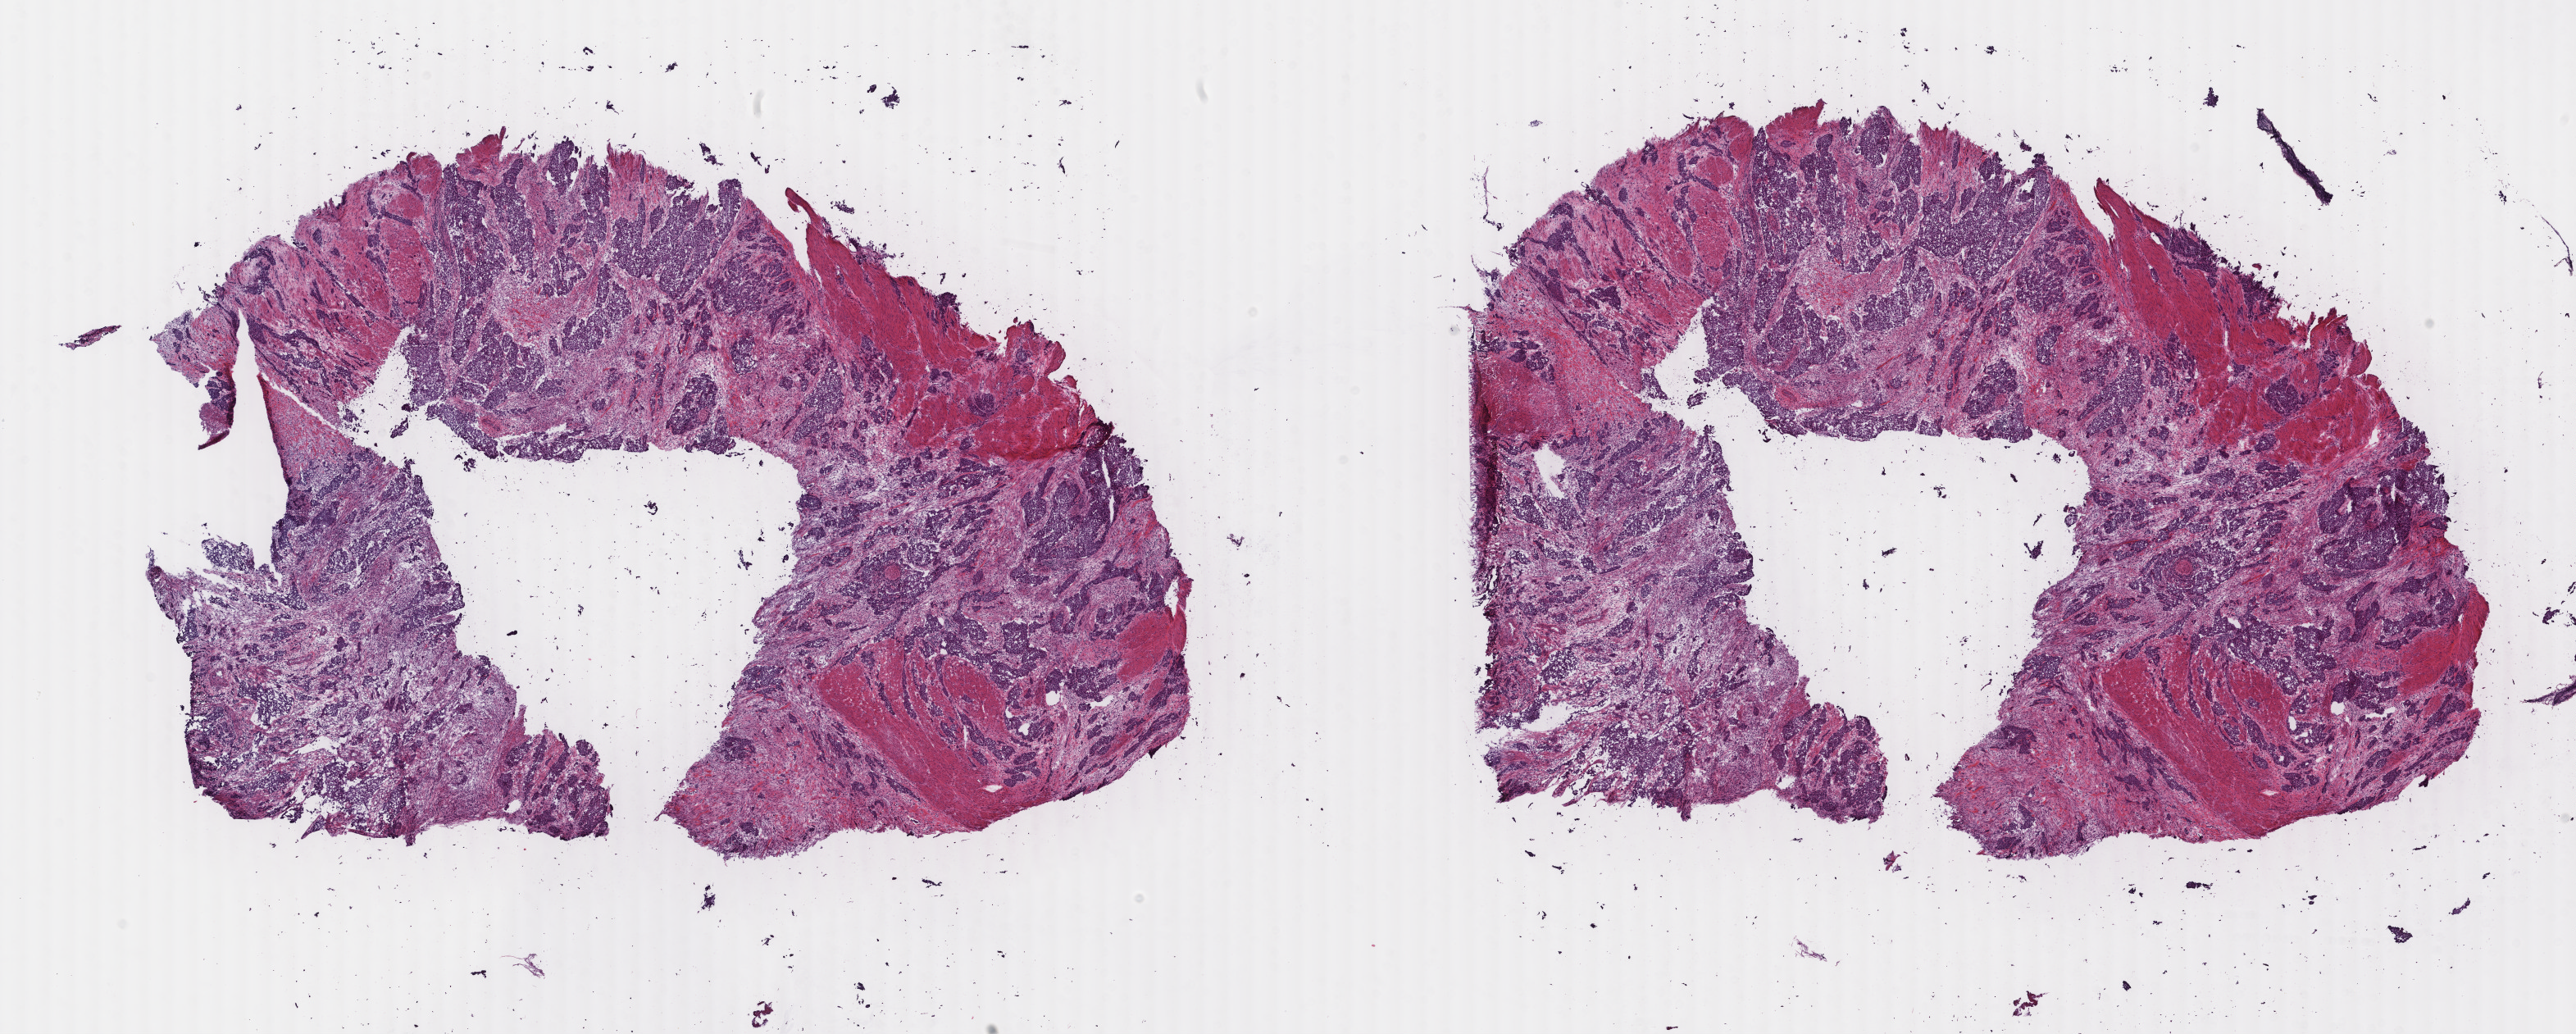
Hematoxylin and eosin (H&E) stained whole-slide image — low-resolution overview of the scanned area, about 25.0 x 10.0 mm, frozen section, bladder, primary tumour sample. Male, age 65 years at initial diagnosis. Histologic grade: high grade. Composition of this section per pathologist review: tumour cells 65%, tumour nuclei 84%, normal cells 0%, stromal cells 35%, necrosis 0%. Infiltration values recorded for this section: lymphocyte infiltration 2%, monocyte infiltration 0%, neutrophil infiltration 0%.
* pathologic diagnosis: Transitional cell carcinoma (posterior wall of bladder)
* lymph nodes positive (case pathology): 2 of 11 examined
* TNM: T4 N2 M0
* AJCC pathologic stage: IV